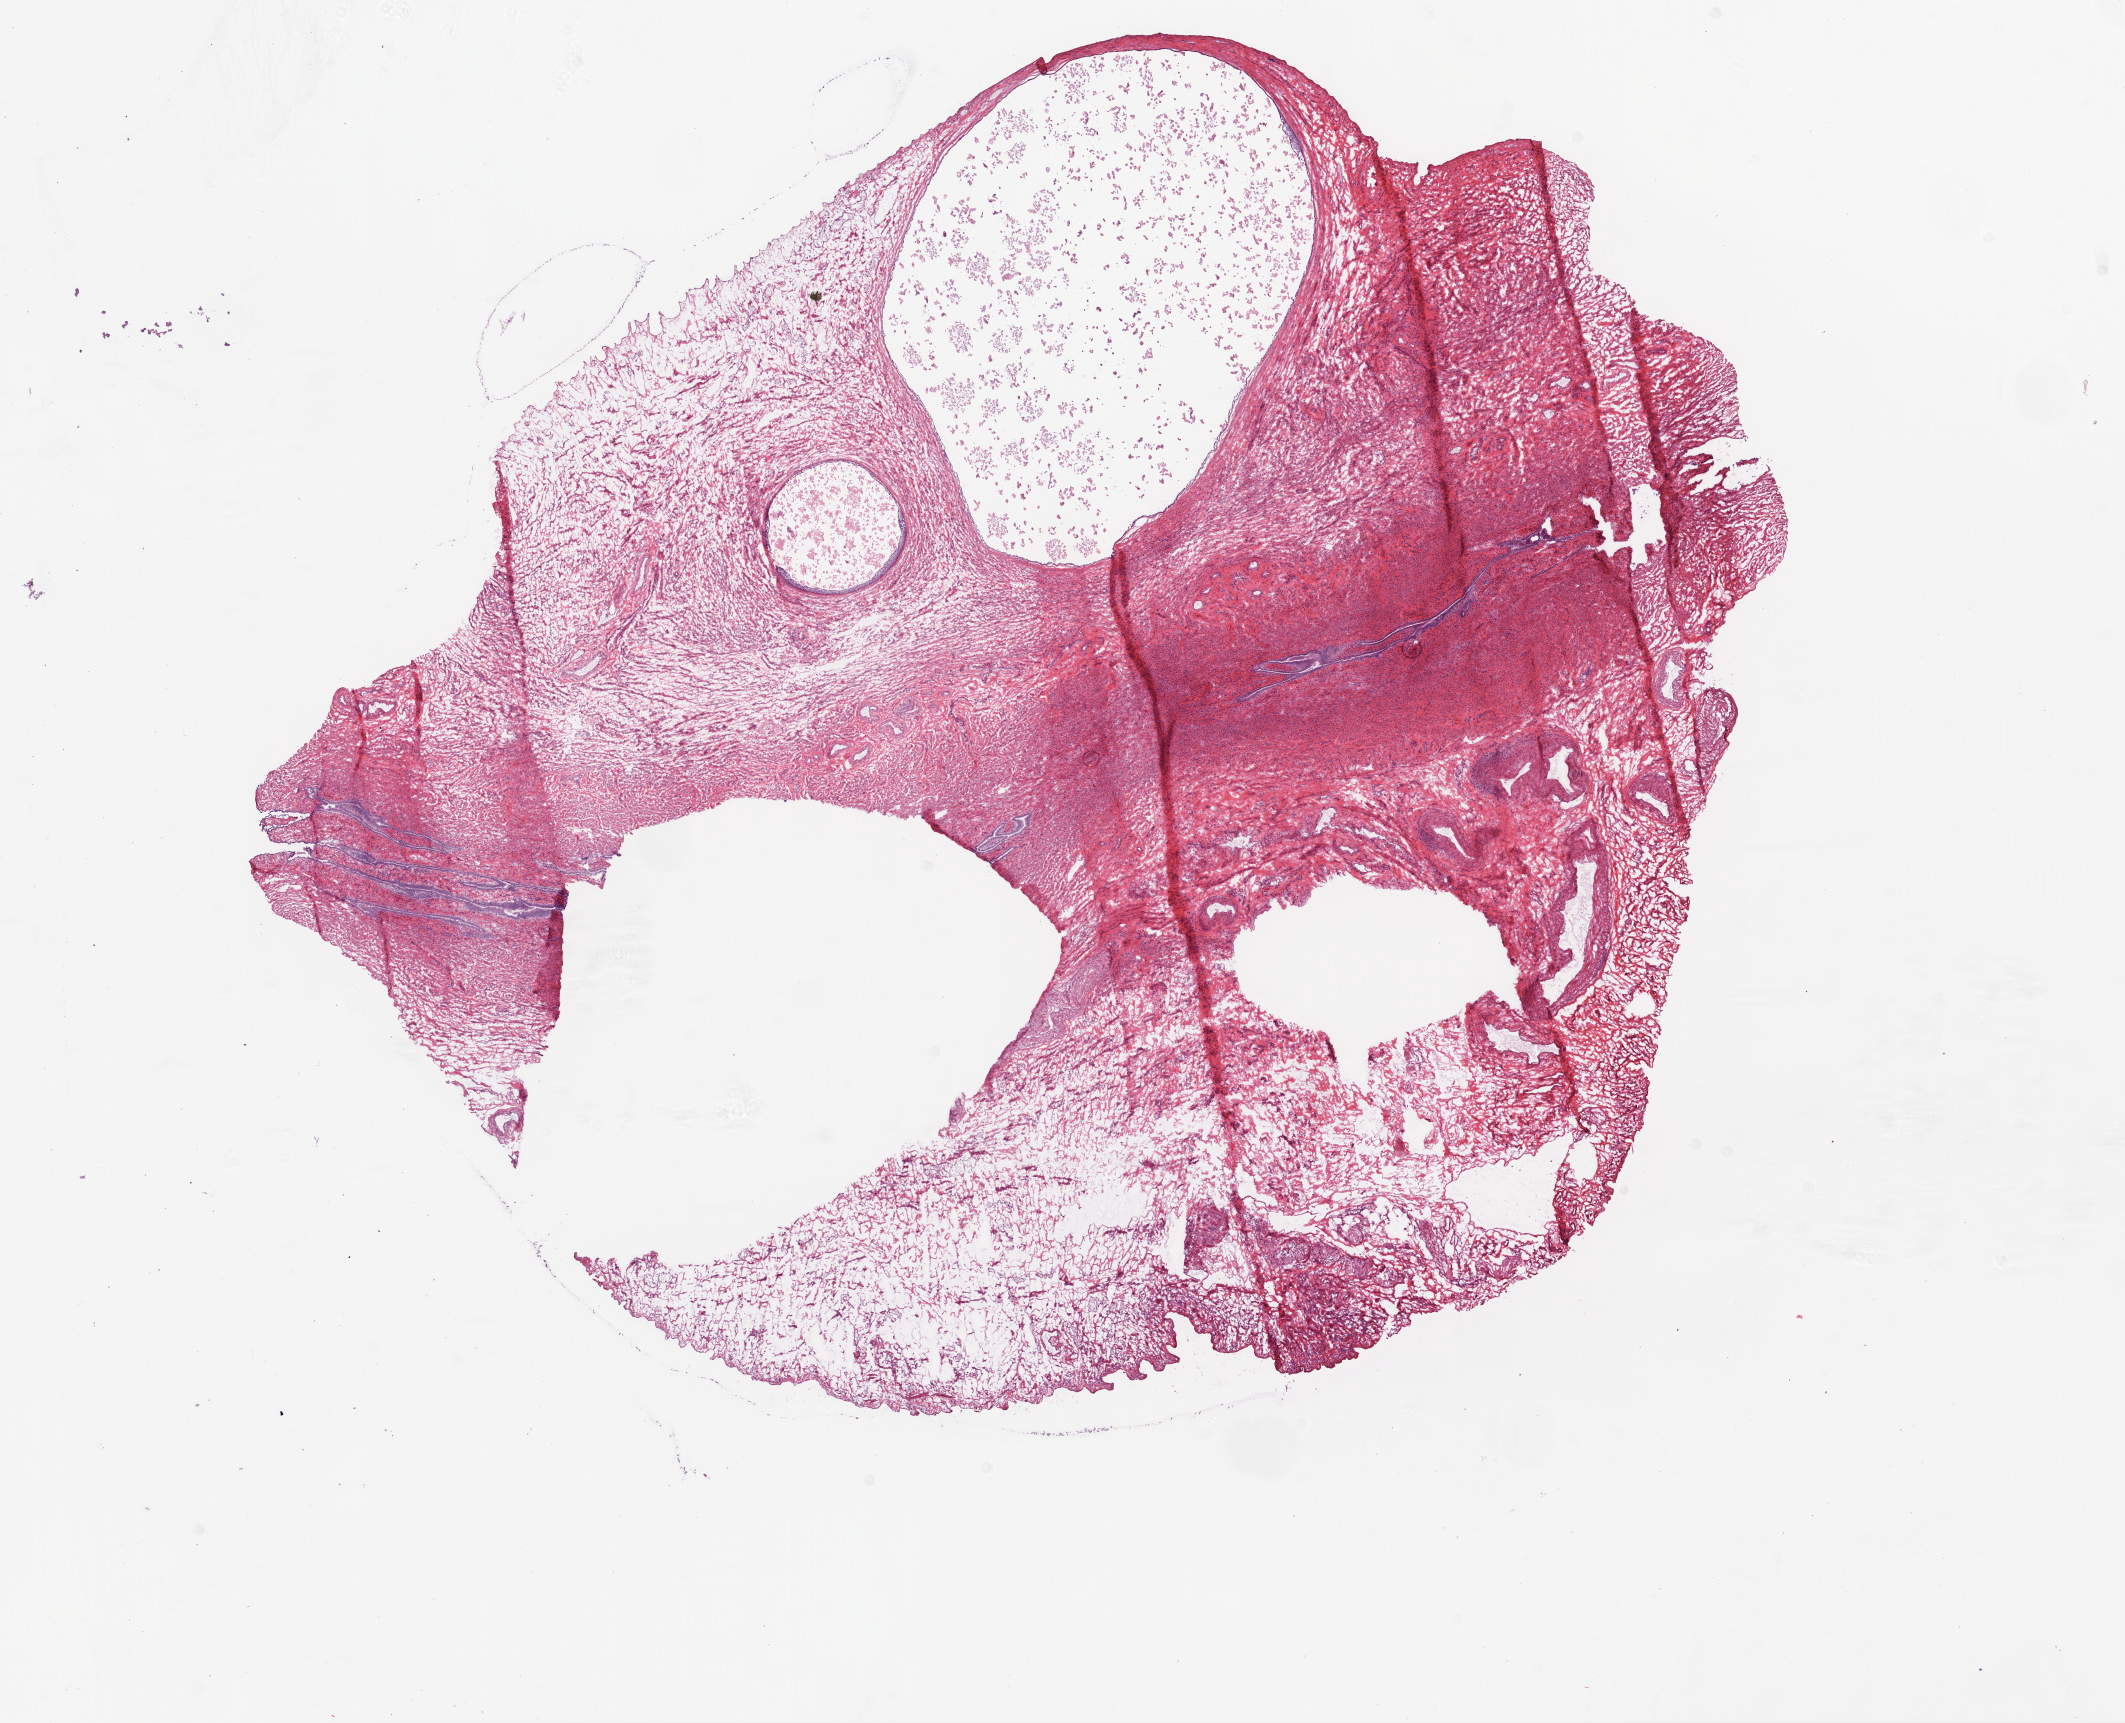
Digitized Hematoxylin and eosin (H&E) stained tissue section (whole slide), low-resolution overview of the scanned area, about 17.1 x 13.8 mm (slide scanned at 20x); frozen section from the bottom of the tissue portion; sample: solid tissue normal (non-tumour tissue), ovary. Patient: female, age at initial diagnosis 63 years.
- this section: solid tissue normal sample (biorepository sample class)
- patient diagnosis: Serous cystadenocarcinoma, NOS